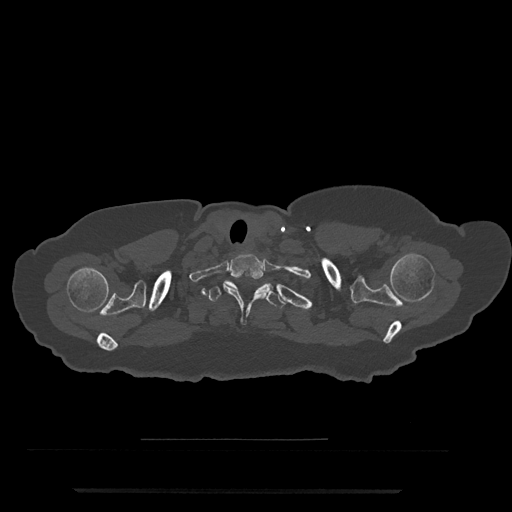
CT including the spine, one axial slice; slice 697 of 797 in the series (ordered by position); reconstruction kernel Br40s/3; bone window (W 1800 / L 400 HU); 0.5 mm slice thickness; 512 × 512 image matrix, field of view 440 × 440 mm. Patient: female, 51 years. Case-level facts recorded for this patient, not image findings: primary cancer: neuro; vertebrae with lytic lesions (as recorded): T8.
Outlined on this slice (semi-automatic segmentation, software-assisted and operator-edited):
- T1 vertebra: bounding box [x1, y1, x2, y2] px = [198, 254, 267, 316]
- T2 vertebra: [208, 280, 286, 309]